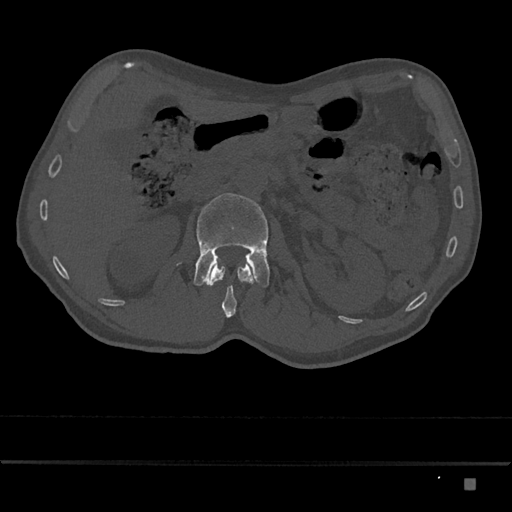
CT including the spine, one axial slice; slice 503 of 797 in the series (ordered by position); bone window (W 1800 / L 400 HU); 0.5 mm slice thickness; 512 × 512 image matrix, field of view 390 × 390 mm. Male patient, age 72 years. Case-level facts recorded for this patient, not image findings: primary cancer: prostate.
Outlined on this slice (semi-automatic segmentation, software-assisted and operator-edited):
- L1 vertebra: bounding box (x1, y1, x2, y2) in pixels: (206, 261, 255, 318)
- L2 vertebra: (176, 193, 270, 287)